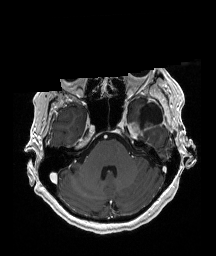
Brain MRI from a brain-tumour surgery series, one axial slice. Position 139 of 192 along the scan axis. T1-weighted post-contrast. 216 × 256 image matrix, field of view 211 × 250 mm. From the clinical record (not read from this slice): histopathology: Glioblastoma; WHO grade: 4; IDH mutation: no.
Structures marked on this image (expert manual segmentation):
- previous resection cavity: bounding box (x1, y1, x2, y2) in pixels: (139, 103, 162, 125)